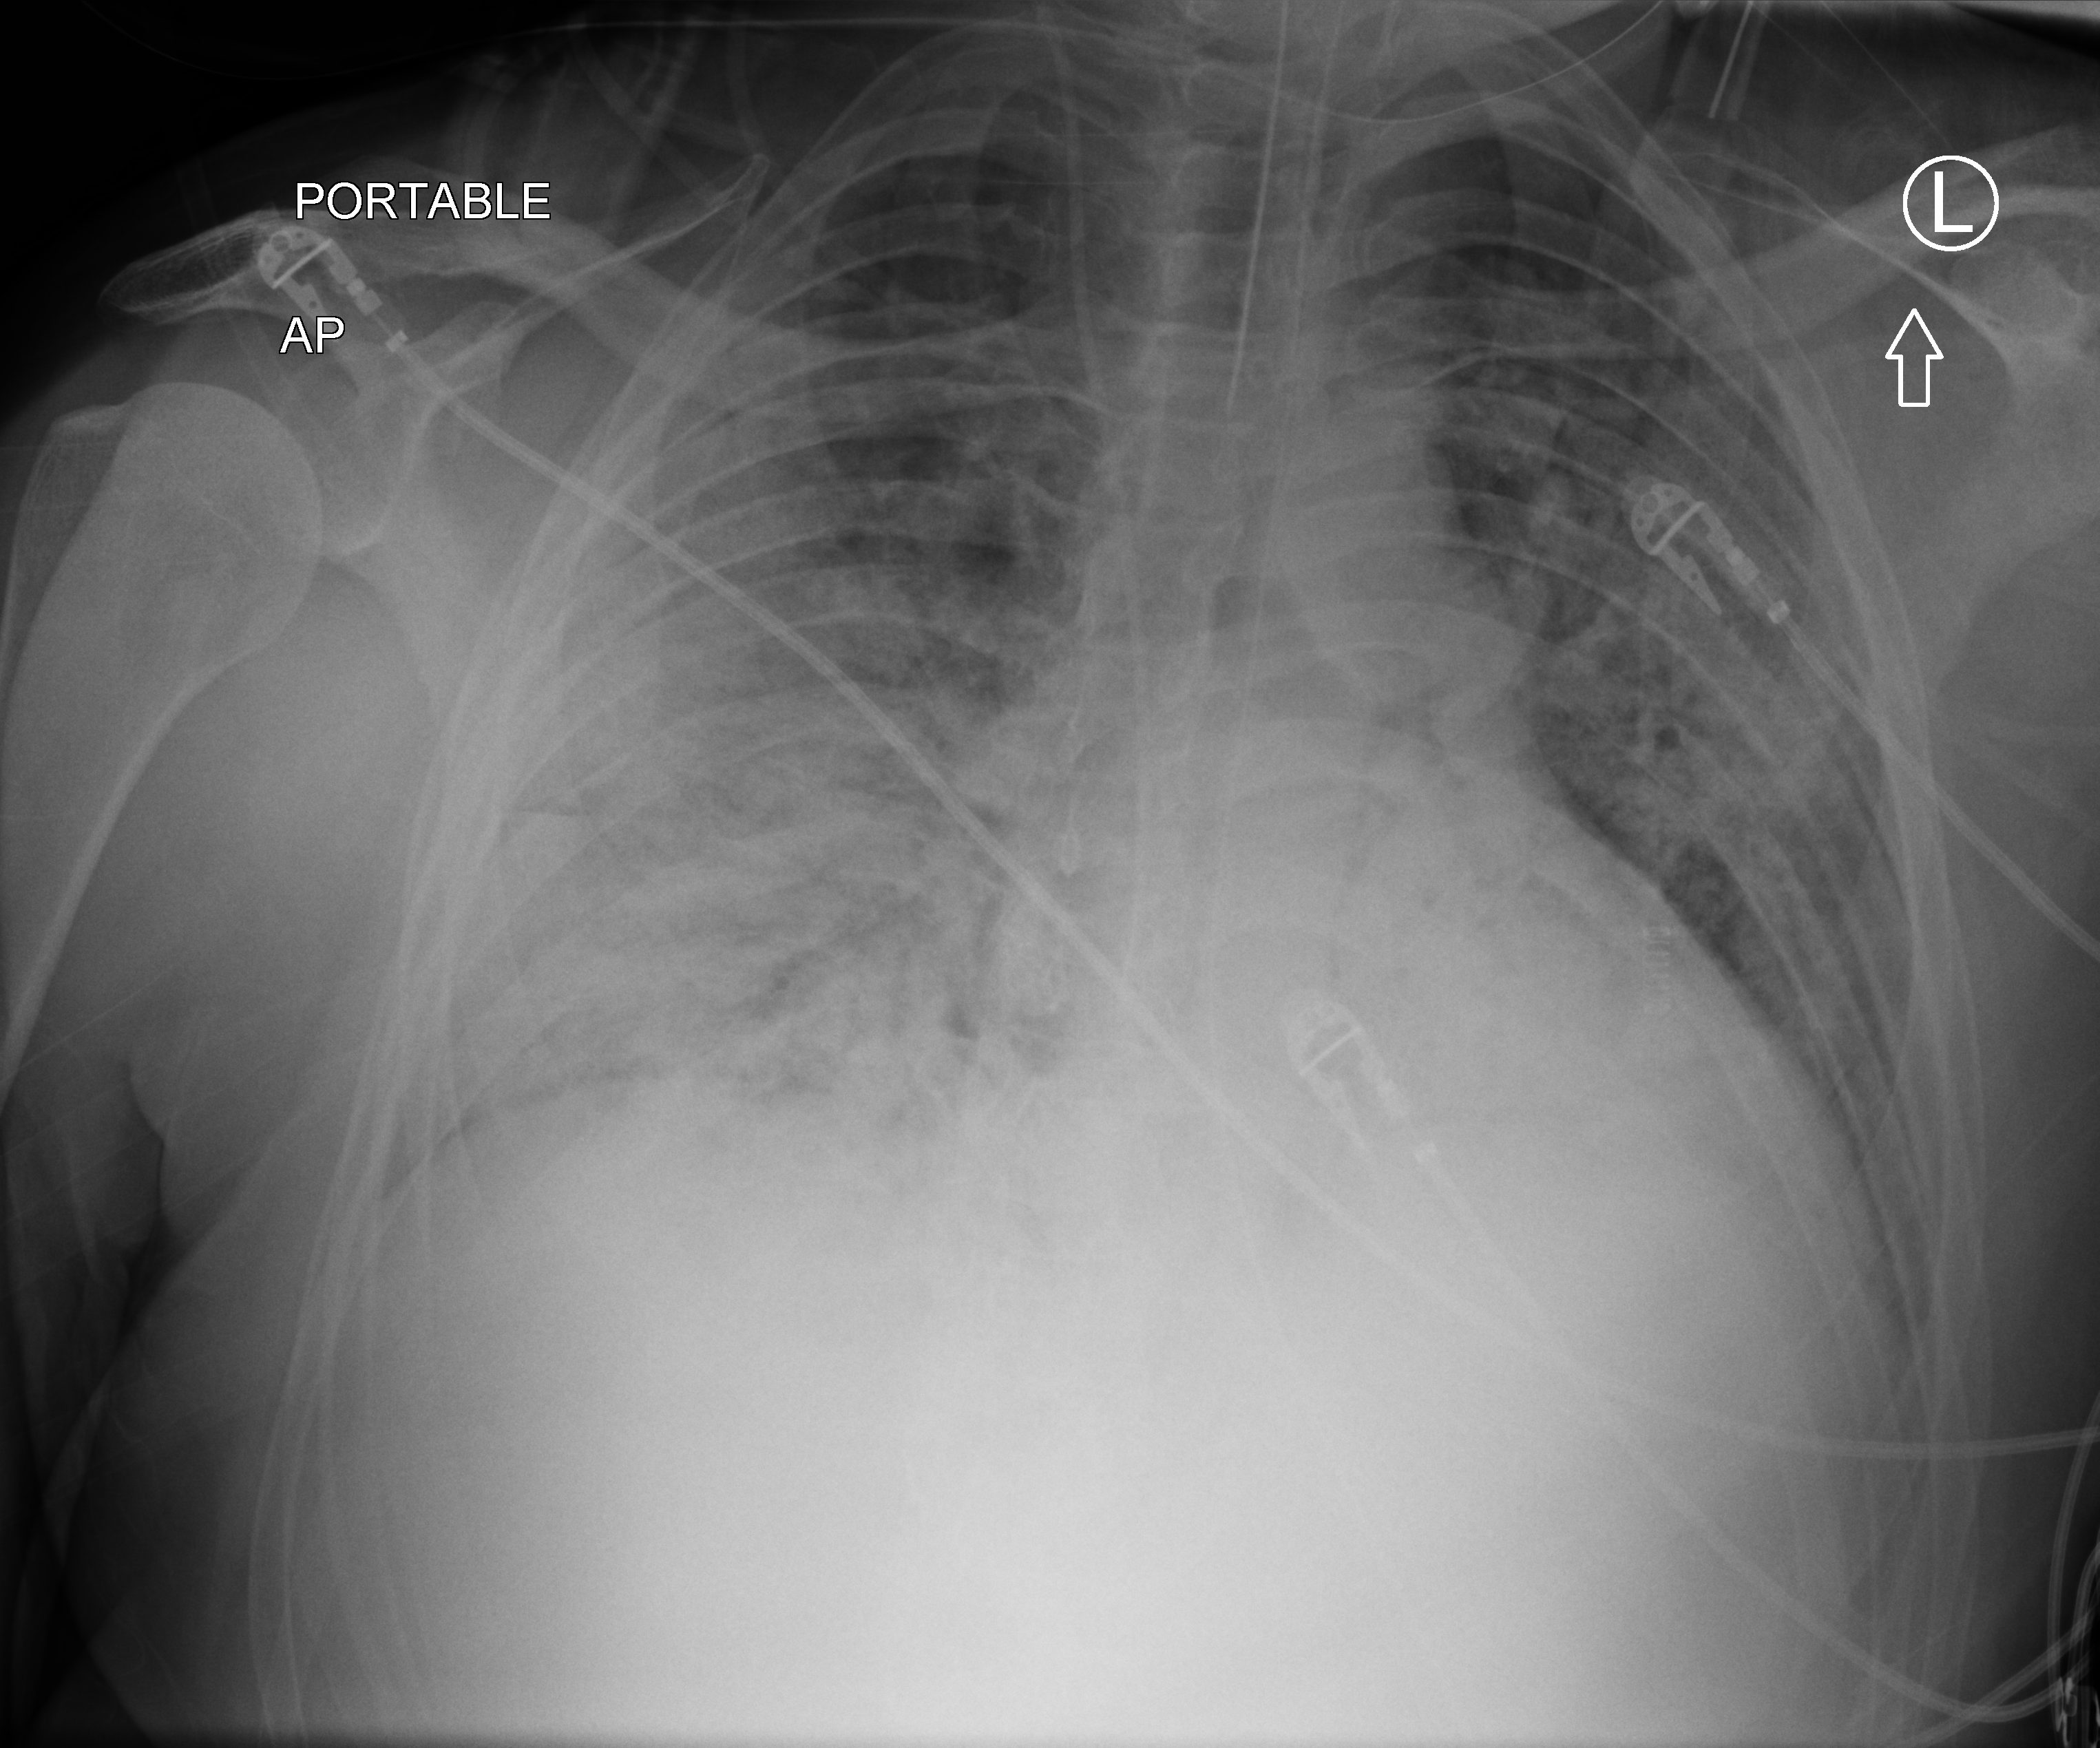
Bedside chest radiograph (computed radiography); anteroposterior (AP) projection. Patient hospitalised with COVID-19; male, aged 18–59 years.
From the hospital-stay record, not from the radiograph (when in the stay this image was taken is not recorded): mechanically ventilated during this hospital stay: yes; admitted to intensive care during this hospital stay: yes.